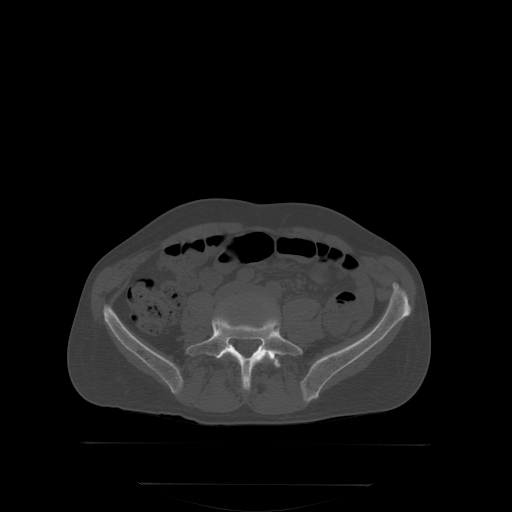
CT including the spine, one axial slice; position 98 of 350 along the scan axis; bone window (W 1800 / L 400 HU); 2.5 mm slice thickness; 512 × 512 image matrix, field of view 500 × 500 mm. Patient: male, 58 years. From the clinical record (not read from this slice): primary cancer: prostate; vertebrae with lytic lesions (as recorded): L1.
Annotated regions visible in this slice (semi-automatically segmented with operator editing):
- L4 vertebra: bounding box (x1, y1, x2, y2) in pixels: (223, 351, 273, 362)
- L5 vertebra: (187, 314, 303, 390)